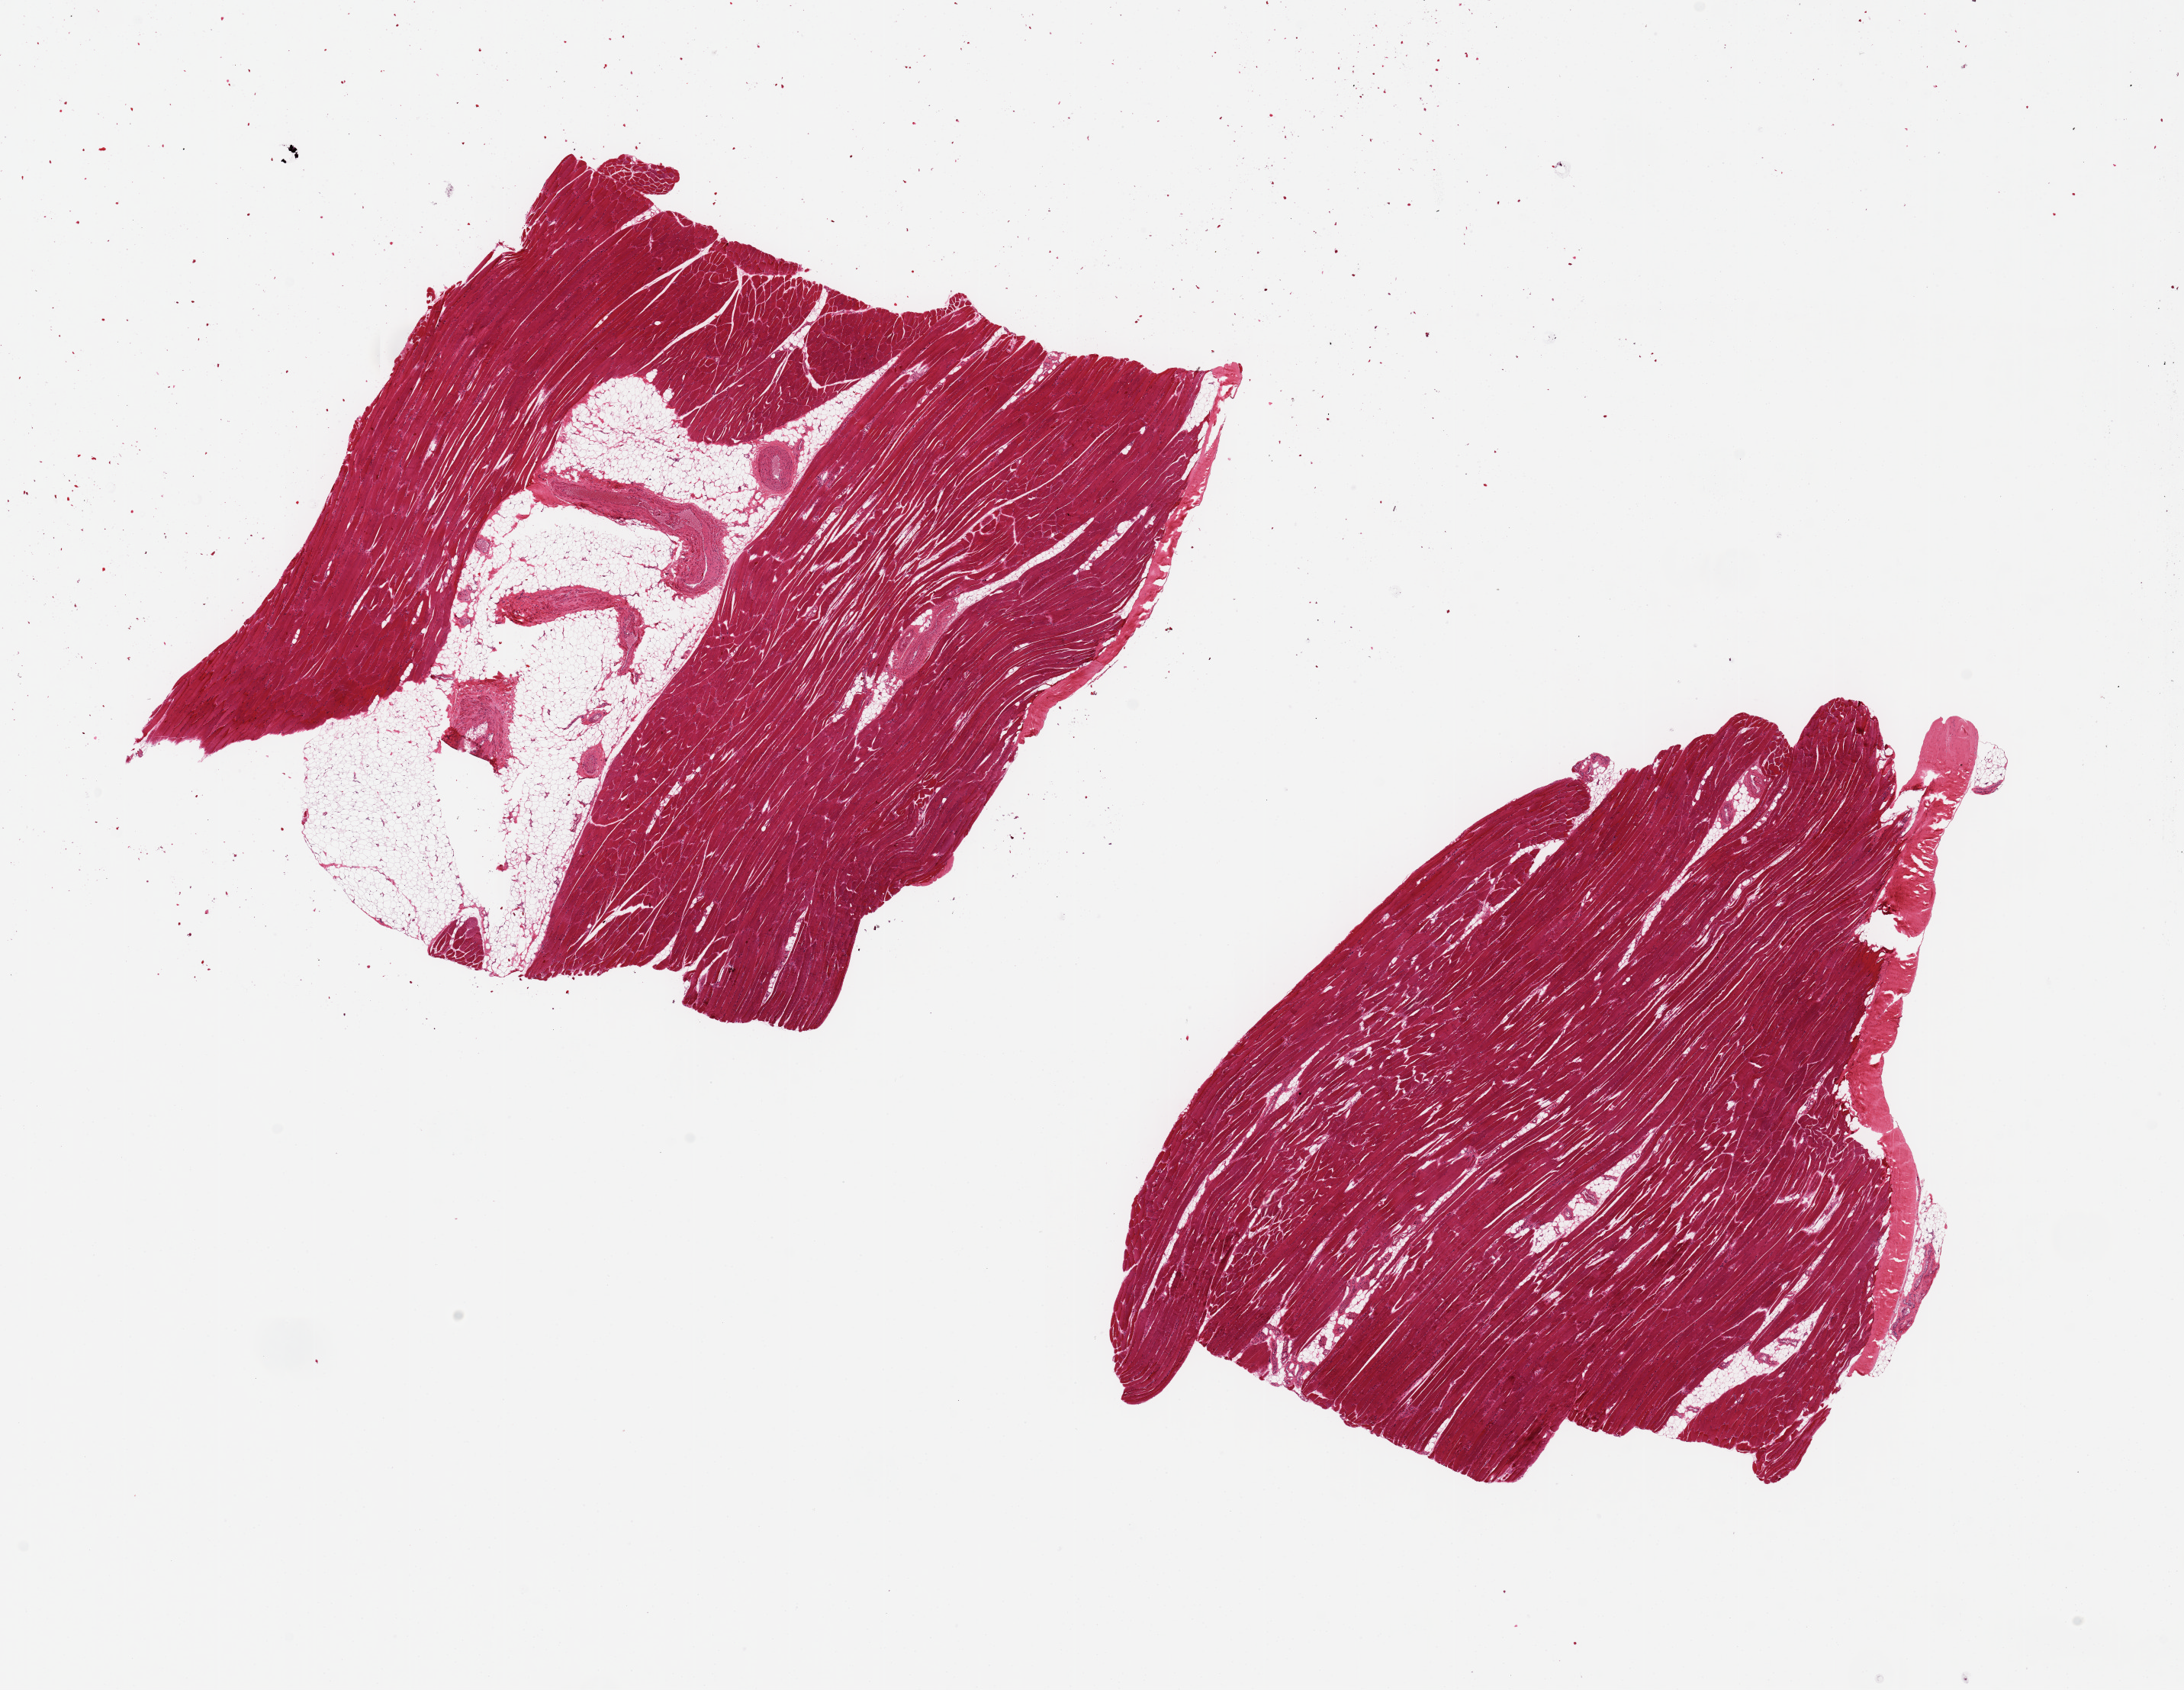
Digitized H&E-stained section, low-resolution overview of the scanned area, about 22.6 x 17.5 mm (acquisition: 20x scan); PAXgene-fixed, paraffin-embedded tissue; sampled site (target tissue): skeletal muscle; donor tissue sample. Donor sex: female.
- review note (as recorded): 2 pieces ~ 8x8mm, one with ~30% interstitial fatty aggregate